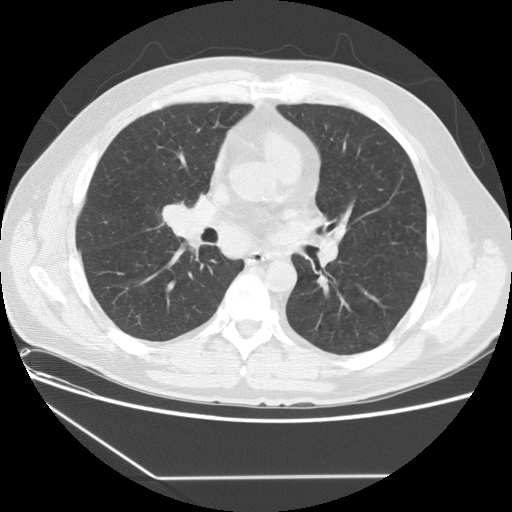
Low-dose screening chest CT, one axial slice; position 80 of 154 along the scan axis; reconstruction kernel STANDARD; lung window (W 1500 / L -600 HU); 512 × 512 image matrix, field of view 370 × 370 mm.
Structures marked on this image (manually delineated by an expert):
- lesion 1 (tumor, middle lobe of right lung): bounding box (x1, y1, x2, y2) in pixels: (162, 204, 200, 236)